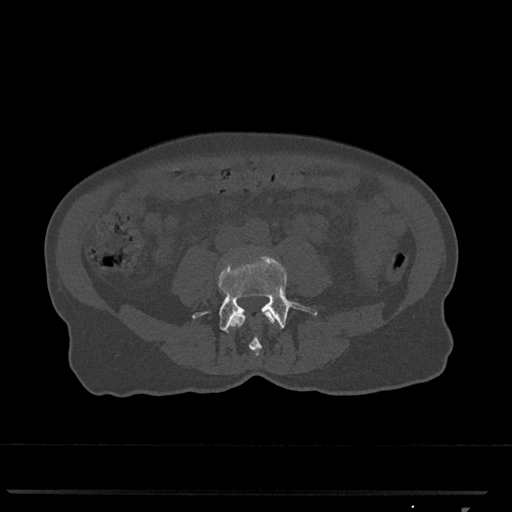
CT including the spine, one axial slice. Position 228 of 793 along the scan axis. Reconstruction kernel Br40s/3. 120 kVp. Bone window (W 1800 / L 400 HU). 512 × 512 image matrix, field of view 380 × 380 mm. Patient: female, 62 years. From the clinical record (not read from this slice): primary cancer: renal.
Structures marked on this image (semi-automatic segmentation, software-assisted and operator-edited):
- L3 vertebra: bounding box (x1, y1, x2, y2) in pixels: (230, 311, 275, 356)
- L4 vertebra: (193, 255, 318, 333)